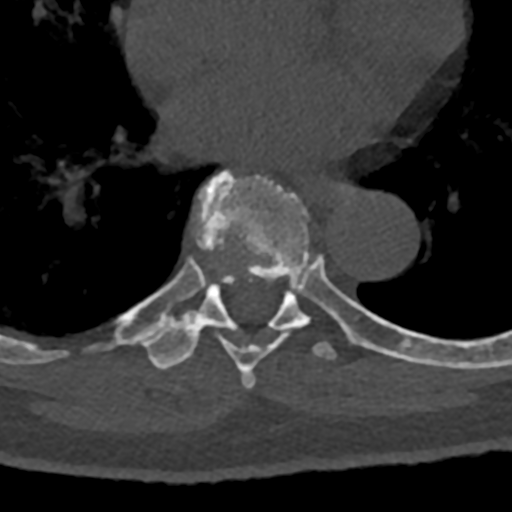
CT including the spine, one axial slice. Slice 736 of 797 in the series (ordered by position). Reconstruction kernel Br40s/3. Bone window (W 1800 / L 400 HU). 0.5 mm slice thickness. 512 × 512 image matrix. Male patient, age 74 years. Case-level facts recorded for this patient, not image findings: primary cancer: renal; vertebrae with lytic lesions (as recorded): T10, L1, L2, L3, L4, L5.
Outlined on this slice (semi-automatic segmentation, software-assisted and operator-edited):
- T7 vertebra: box from (x=196, y=170) to (x=365, y=389) px
- T8 vertebra: (x=100, y=274)–(x=432, y=370)